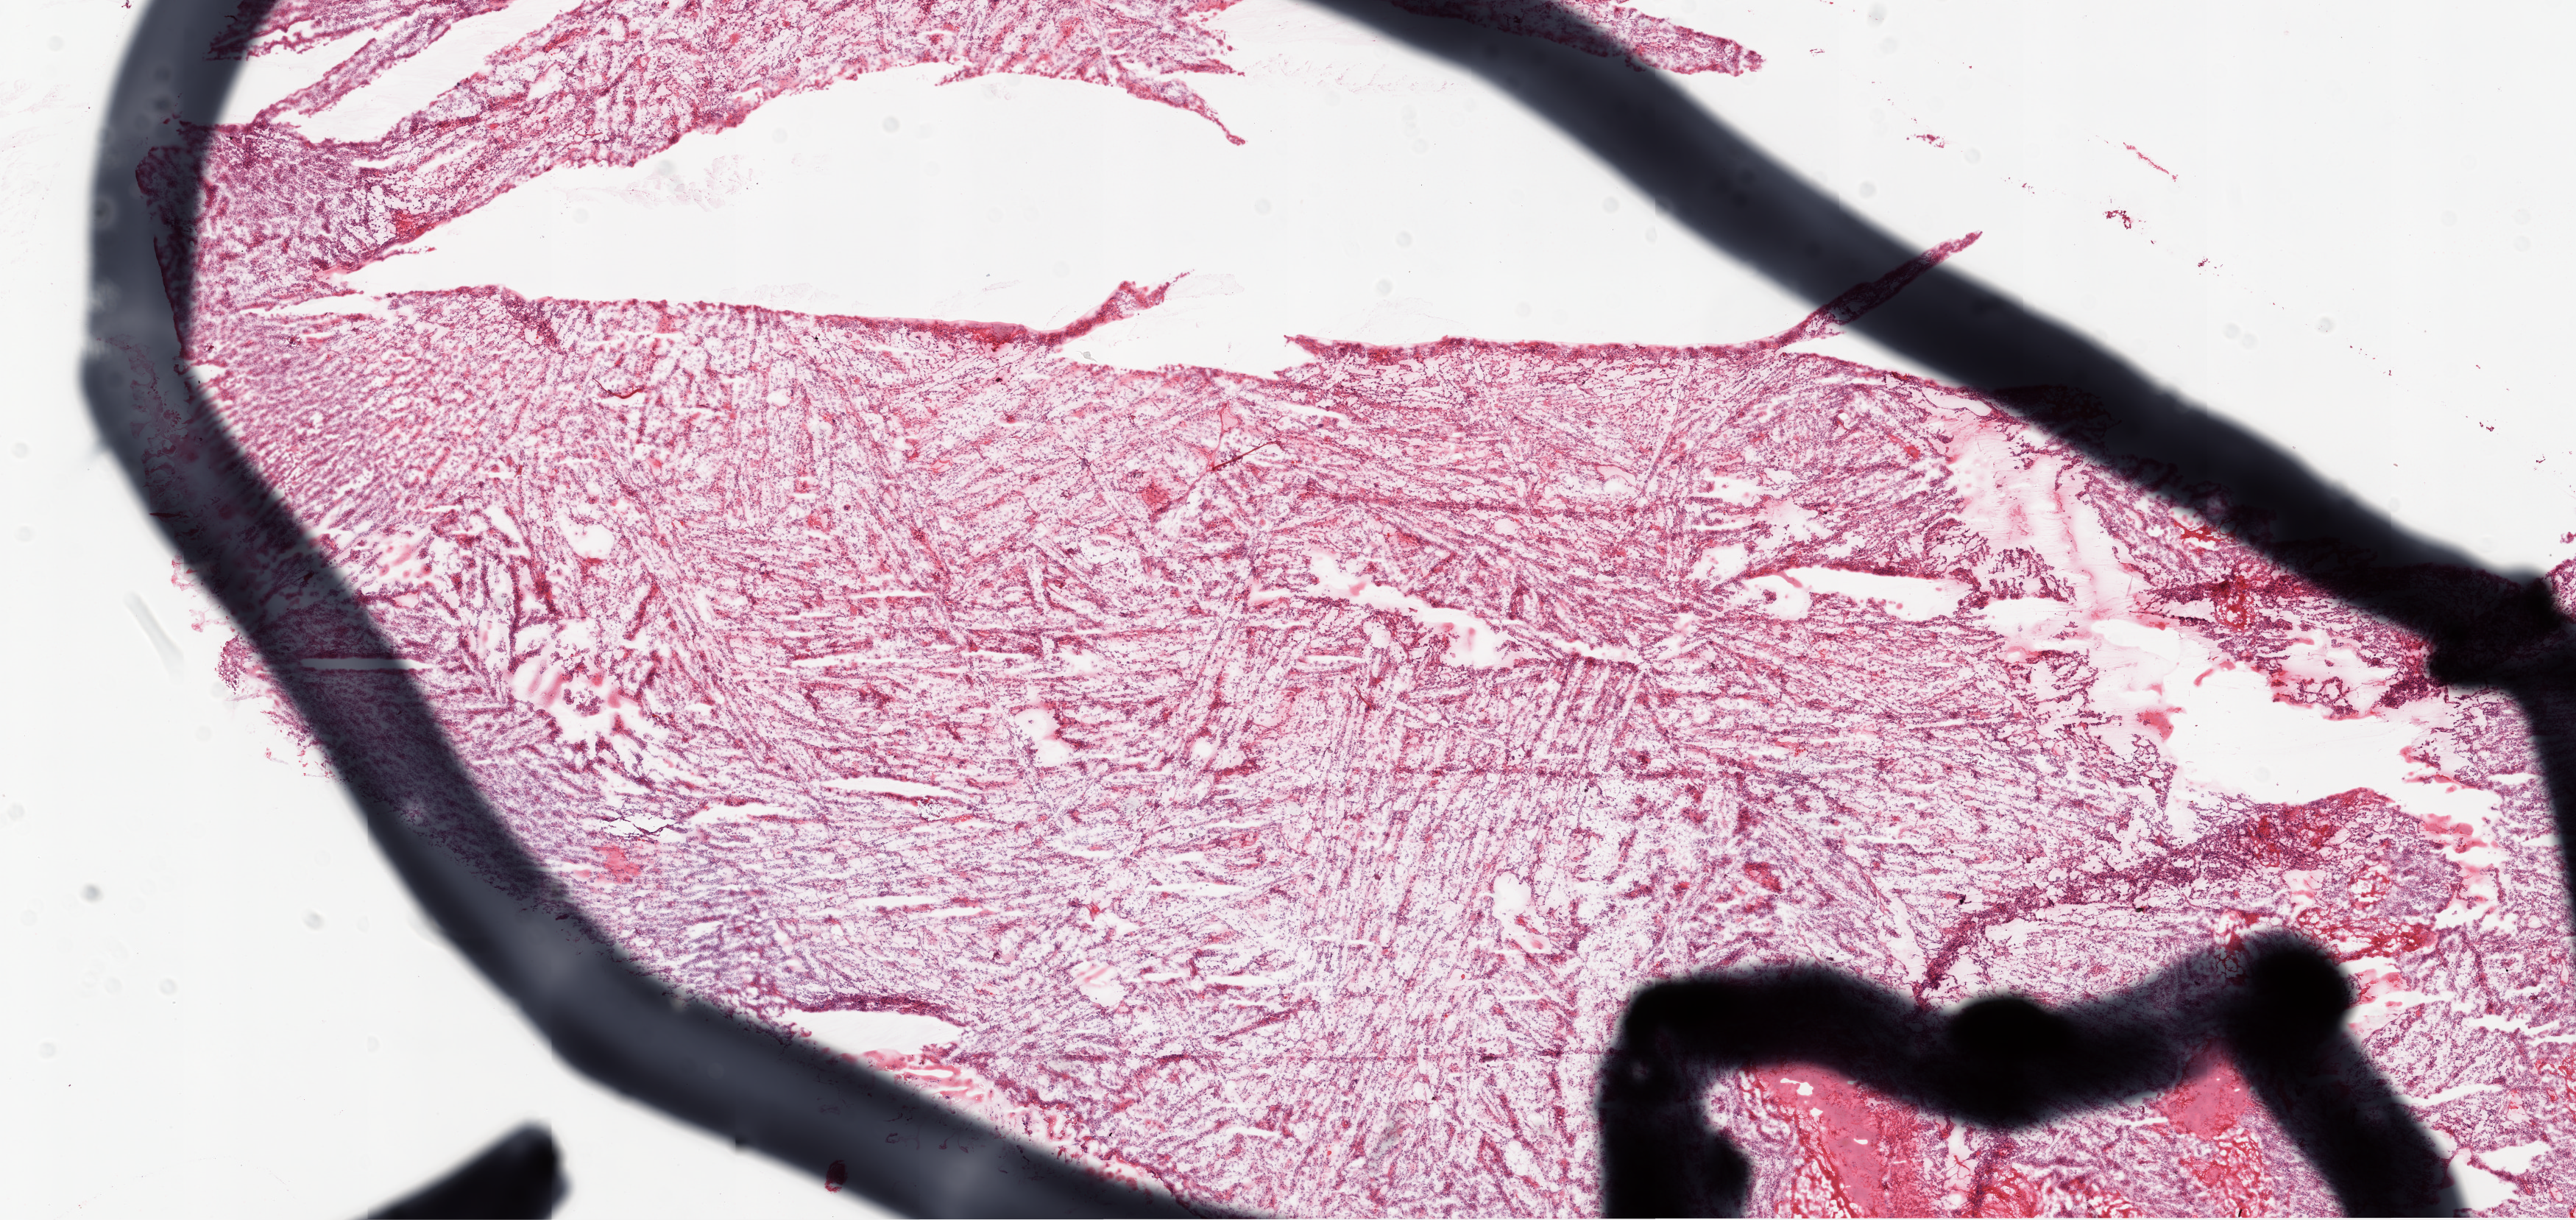
H&E-stained whole-slide image — whole scanned area (about 14.0 x 6.6 mm) shown as a low-resolution overview. Frozen section from the top of the tissue portion. Primary tumour sample from the ovary. Female patient; age at initial diagnosis 74 years.
Histologic diagnosis: Serous cystadenocarcinoma, NOS.